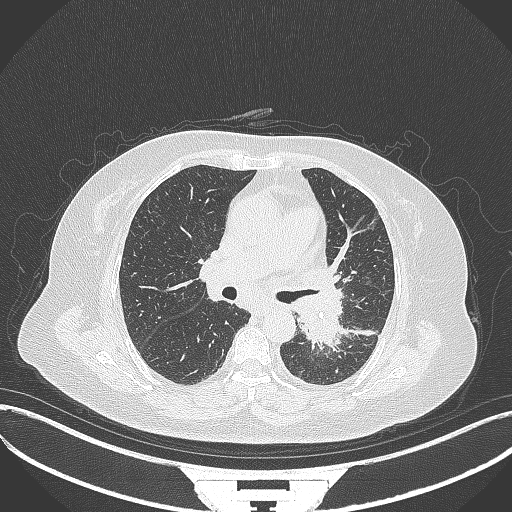
Chest CT, one axial slice. Position 202 of 322 along the scan axis. Reconstruction kernel B70f. 120 kVp. Lung window (W 1500 / L -600 HU). 1 mm slice thickness. 512 × 512 image matrix, field of view 400 × 400 mm. Female patient, age 69 years. From the clinical record (not read from this slice): clinical TNM (as recorded): T2b N3 M1.
Structures marked on this image (rectangle marked by the reading radiologist):
- lung tumour (recorded histology: adenocarcinoma): box from (x=291, y=287) to (x=344, y=353) px